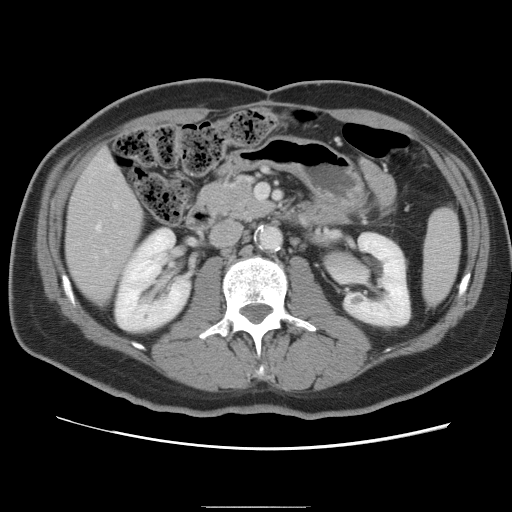
Contrast-enhanced abdominal CT, one axial slice; slice 31 of 87 in the series (ordered by position); intravenous contrast given; soft-tissue window (W 400 / L 40 HU); 5 mm slice thickness; 512 × 512 image matrix, field of view 363 × 363 mm. Male patient, age 63 years. From the clinical record (not read from this slice): diagnosis: colorectal cancer liver metastases, imaged before liver resection; multiple liver metastases: no; largest metastasis: 9 cm; disease in both lobes: no.
Outlined on this slice (outlined manually by an expert reader):
- hepatic veins: box from (x=96, y=223) to (x=101, y=230) px
- liver: (x=67, y=152)–(x=143, y=302)
- planned liver remnant (the part of the liver to remain after resection): (x=67, y=152)–(x=143, y=303)